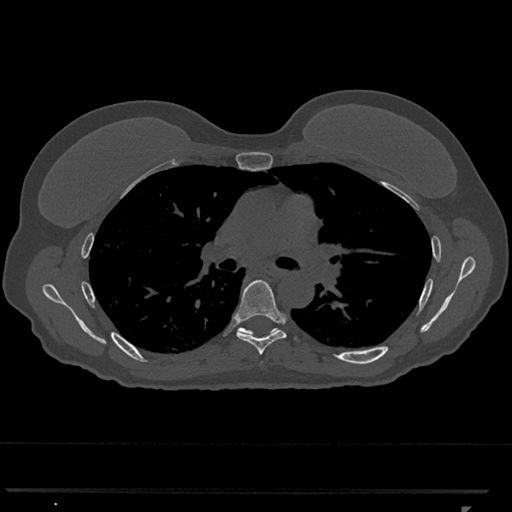
CT including the spine, one axial slice; slice 754 of 793 in the series (ordered by position); 120 kVp; bone window (W 1800 / L 400 HU); 0.5 mm slice thickness; 512 × 512 image matrix, field of view 380 × 380 mm. Female patient, age 62 years. From the clinical record (not read from this slice): primary cancer: renal.
Outlined on this slice (semi-automatic segmentation, software-assisted and operator-edited):
- T6 vertebra: bounding box (x1, y1, x2, y2) in pixels: (235, 279, 286, 355)
- T7 vertebra: (237, 327, 277, 335)